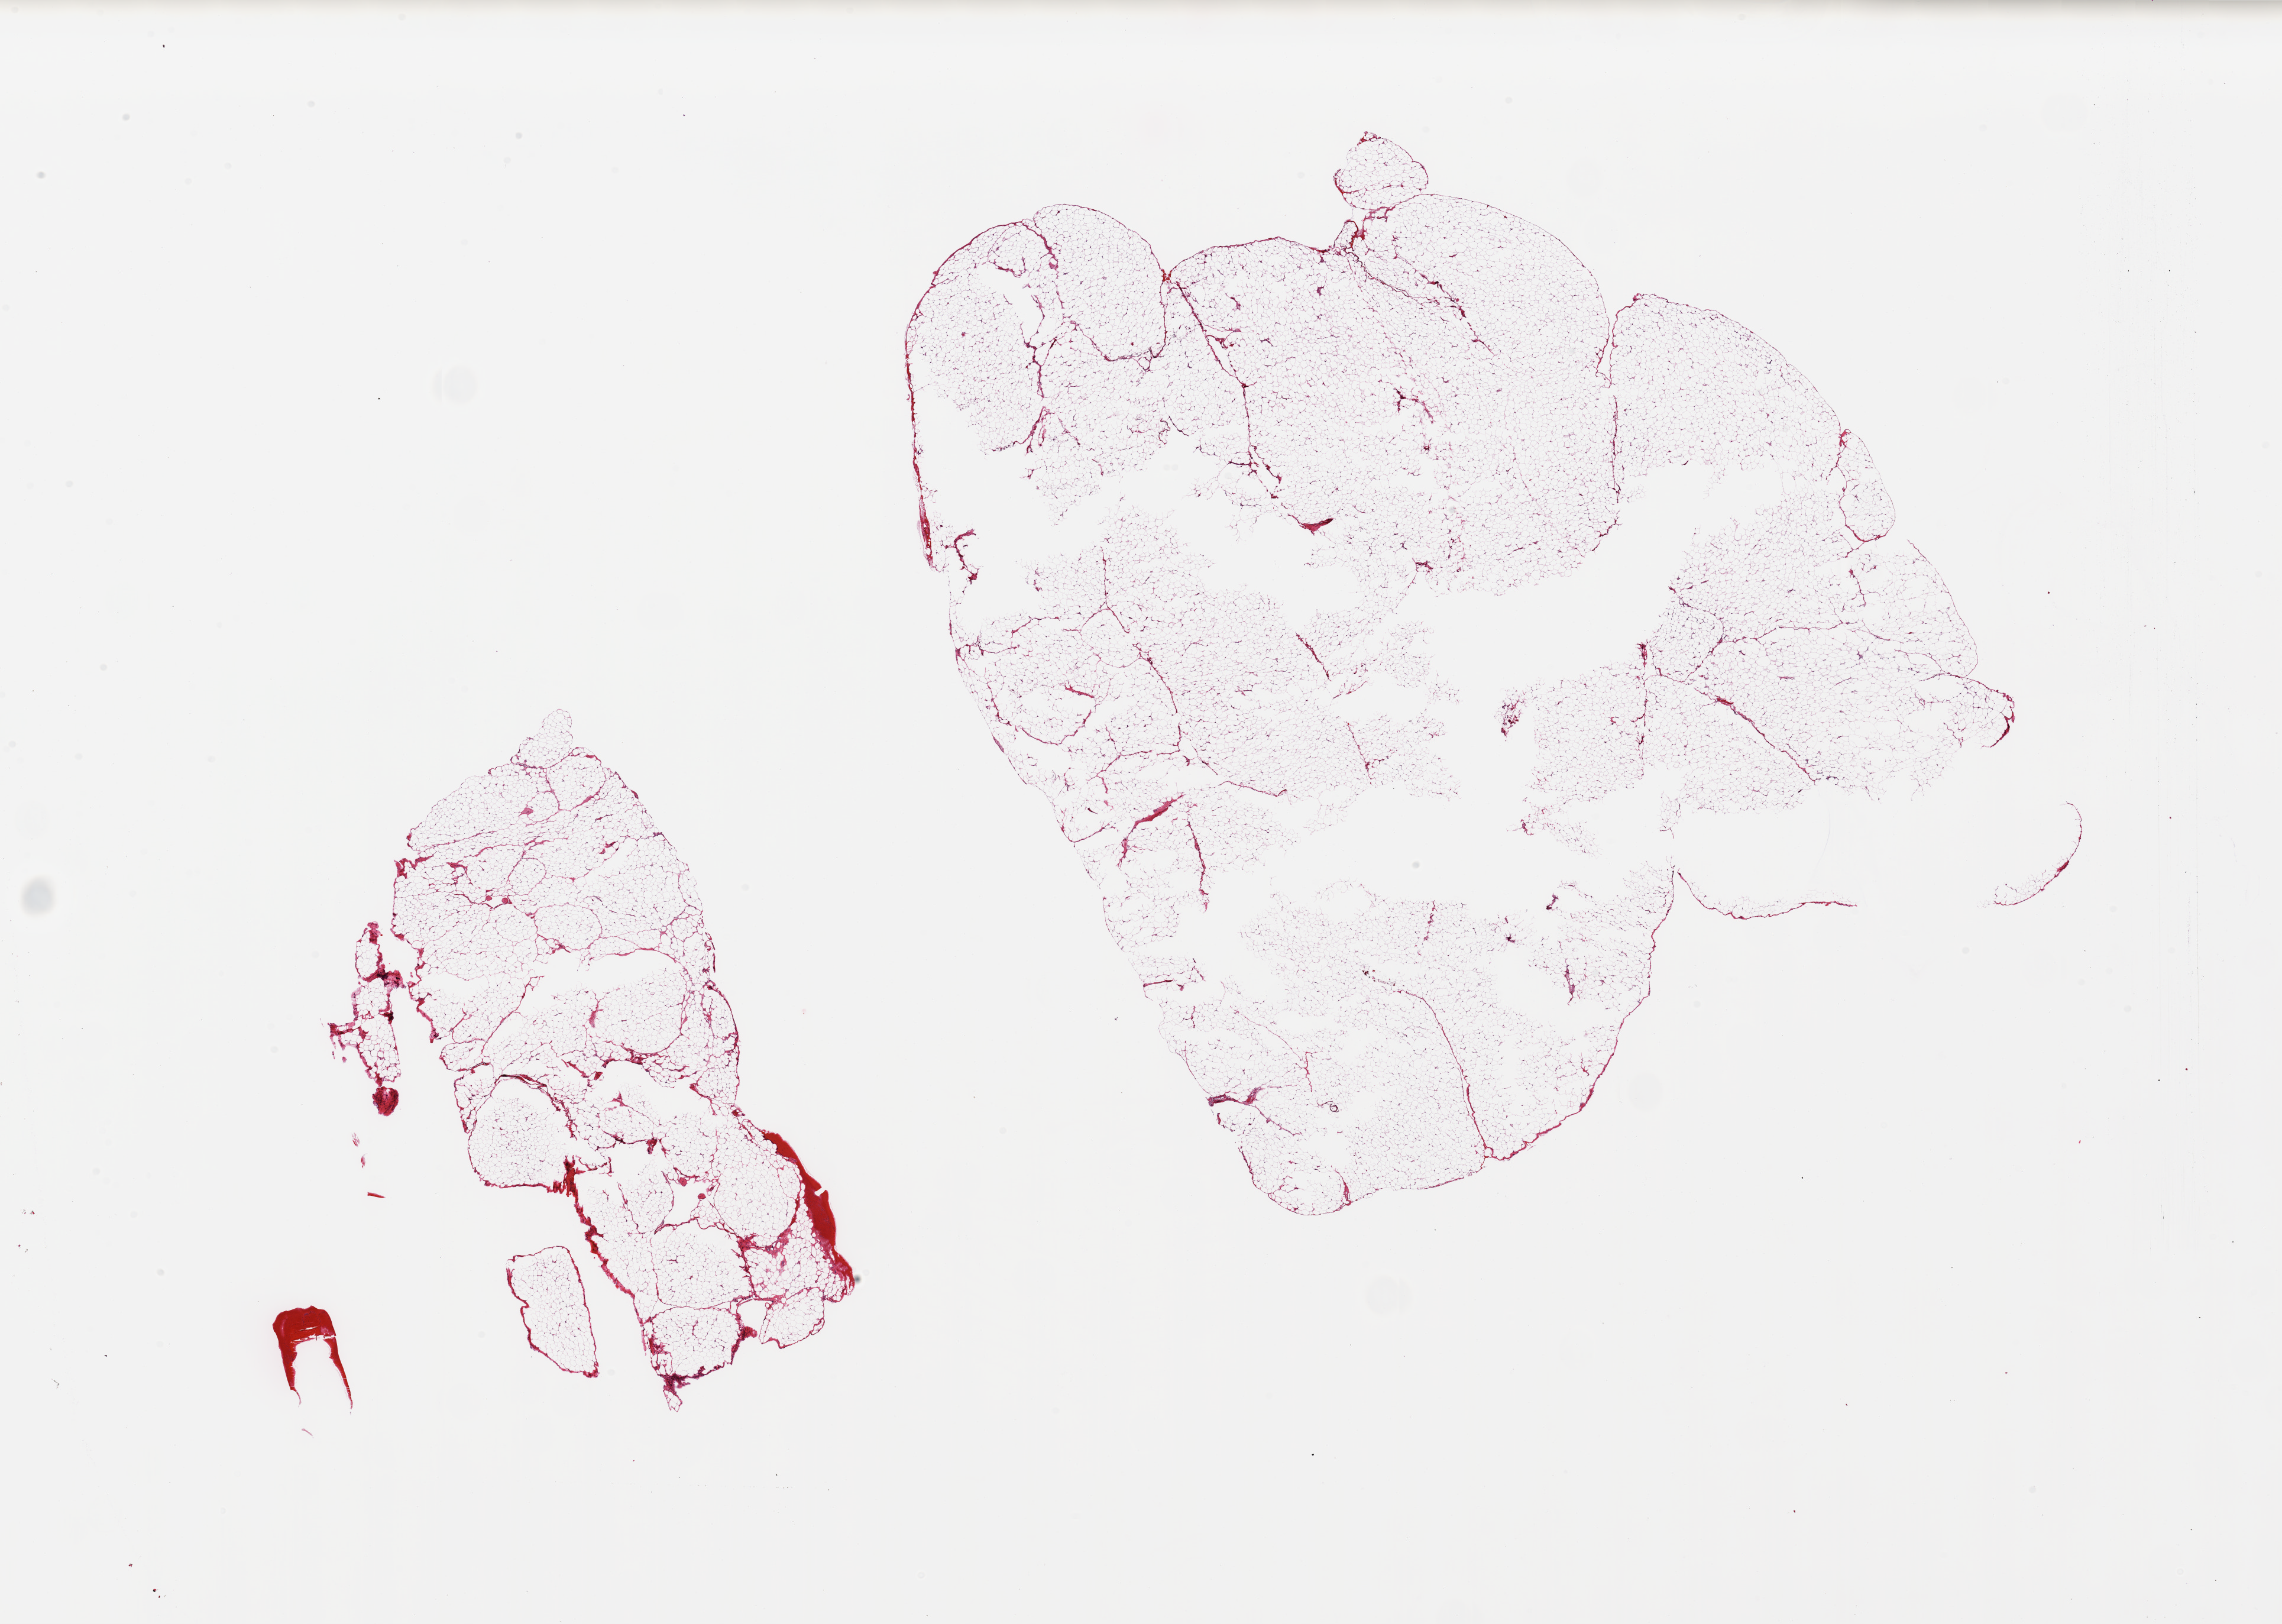
Haematoxylin and eosin whole-slide image, whole scanned area (about 30.5 x 21.7 mm, slide scanned at 20x) shown as a low-resolution overview. PAXgene-fixed paraffin-embedded (PFPE) section. Sampled site (target tissue): omentum. Donor tissue sample. Donor sex: male.
Reviewer comment on this tissue sample: 2 pieces; minimal fibrous content; central defect, possible fracture.